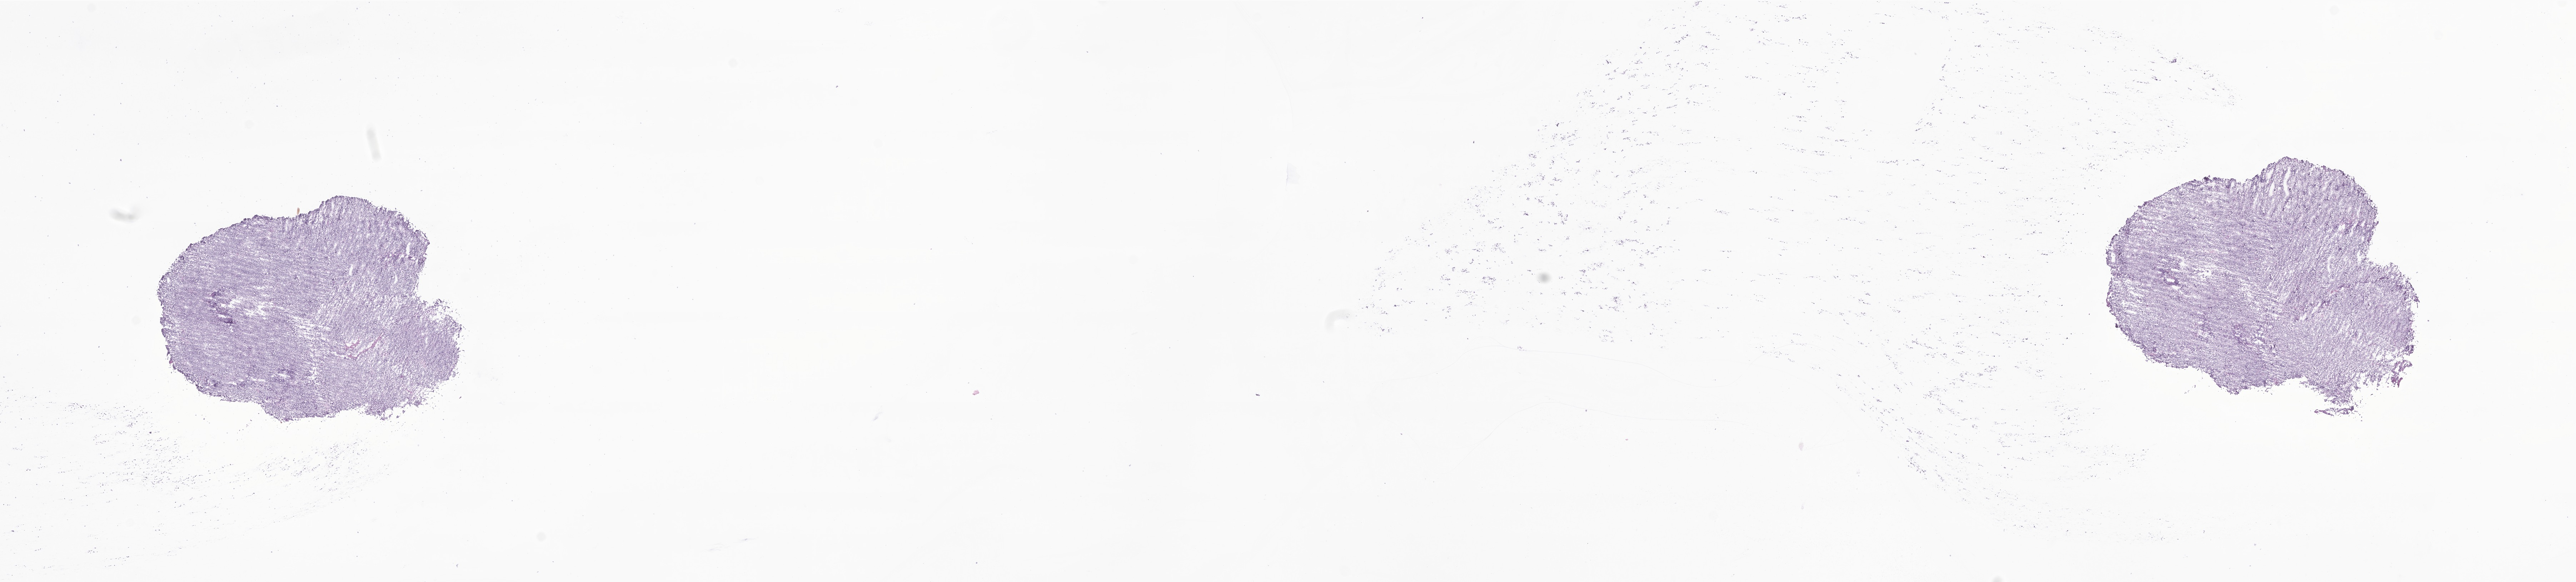
Digitized hematoxylin and eosin (H&E)-stained section of tumor tissue from the brain, shown as a low-resolution overview of the whole scanned area (about 30.4 x 6.9 mm); frozen section (OCT-embedded). Patient male; age 103 months (8 years 7 months).
• diagnosis (ICD-O-3 morphology term): Medulloblastoma, NOS